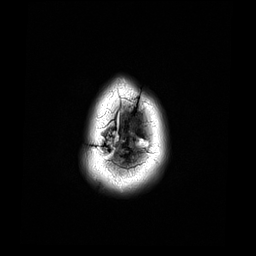
Brain MRI from a brain-tumour surgery series, one axial slice. Position 3 of 44 along the scan axis. 4 mm slice thickness. 256 × 256 image matrix, field of view 240 × 240 mm. From the clinical record (not read from this slice): histopathology: Astrocytoma; WHO grade: 4; IDH mutation: yes; tumour location: Right Frontal.
Annotated regions visible in this slice (manually delineated by an expert):
- tumour: bounding box [x1, y1, x2, y2] px = [108, 142, 112, 147]